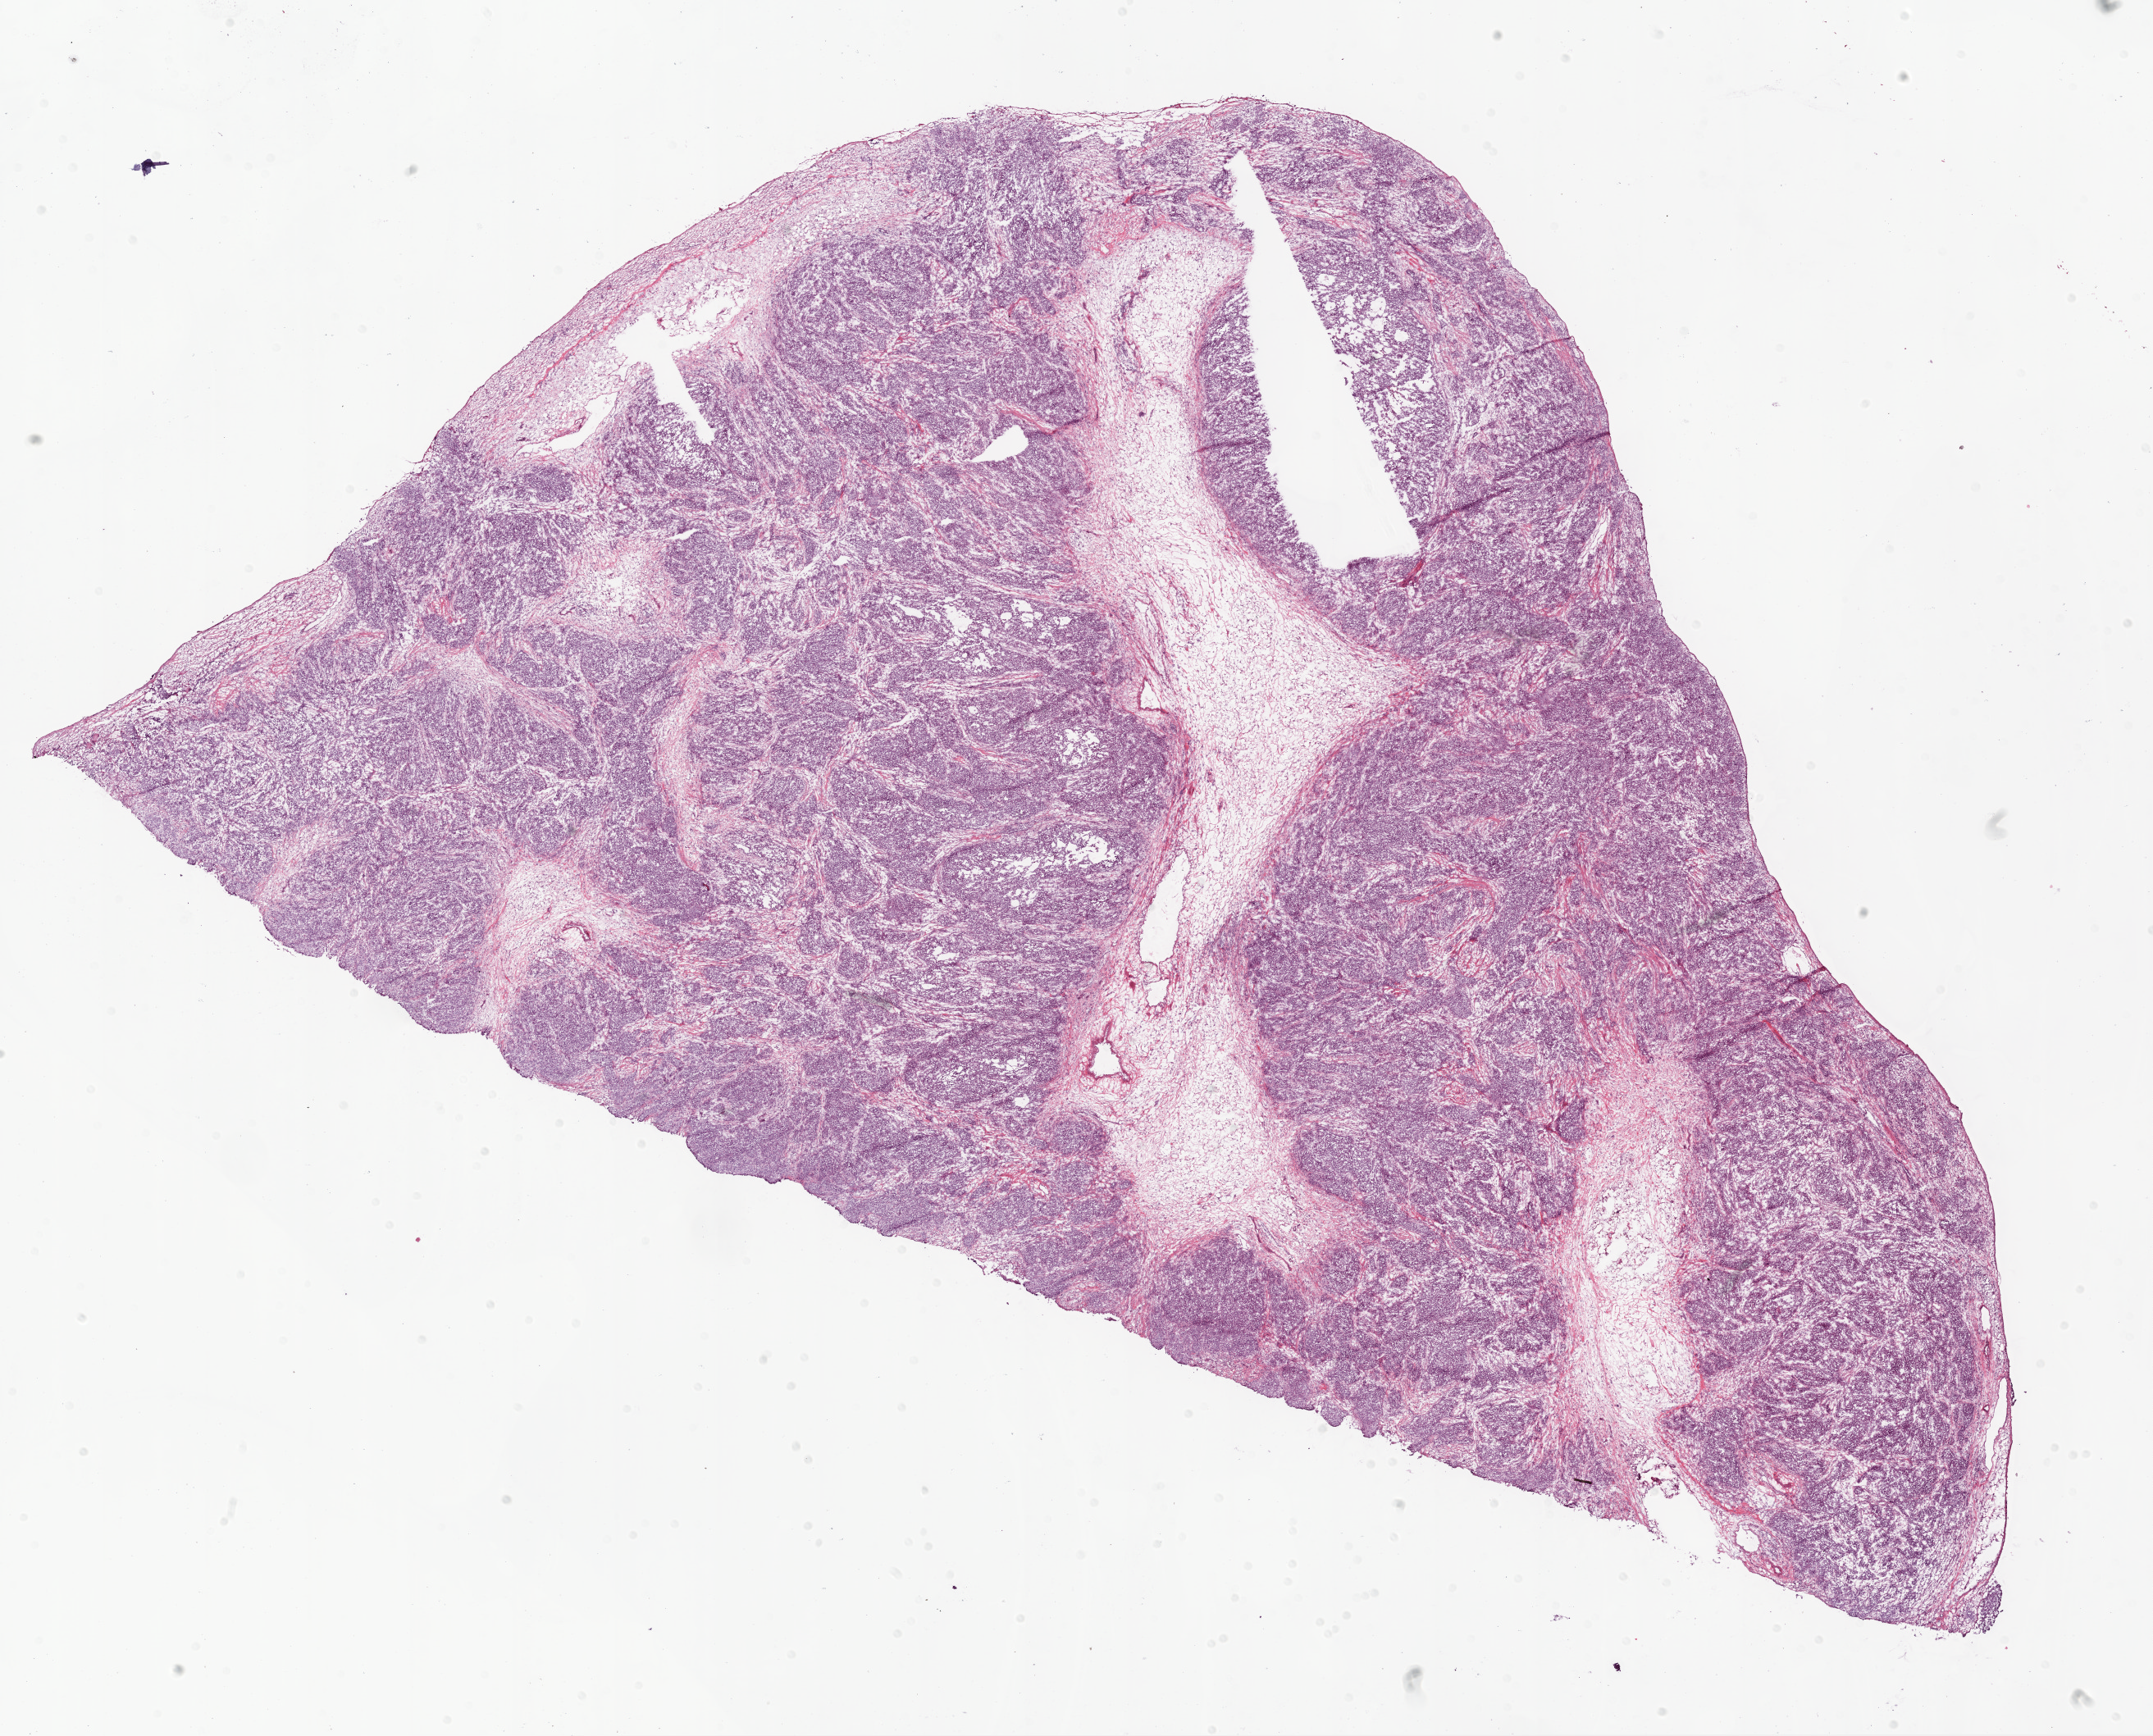
Whole-slide histology image, Hematoxylin and eosin (H&E) stained, shown as a low-resolution overview of the whole scanned area (about 21.1 x 17.0 mm, from a 20x scan). Frozen section. Sample: primary tumour, ovary. Female, age 54 years at initial diagnosis. Histologic grade: G2 (moderately differentiated). Pathologist review of this section (percent, as recorded): tumour cells 85%, tumour nuclei 75%, normal cells 0%, stromal cells 0%, necrosis 15%. Infiltration values recorded for this section: lymphocyte infiltration 15%.
Pathologic diagnosis: Serous cystadenocarcinoma, NOS. FIGO stage: IIIC.